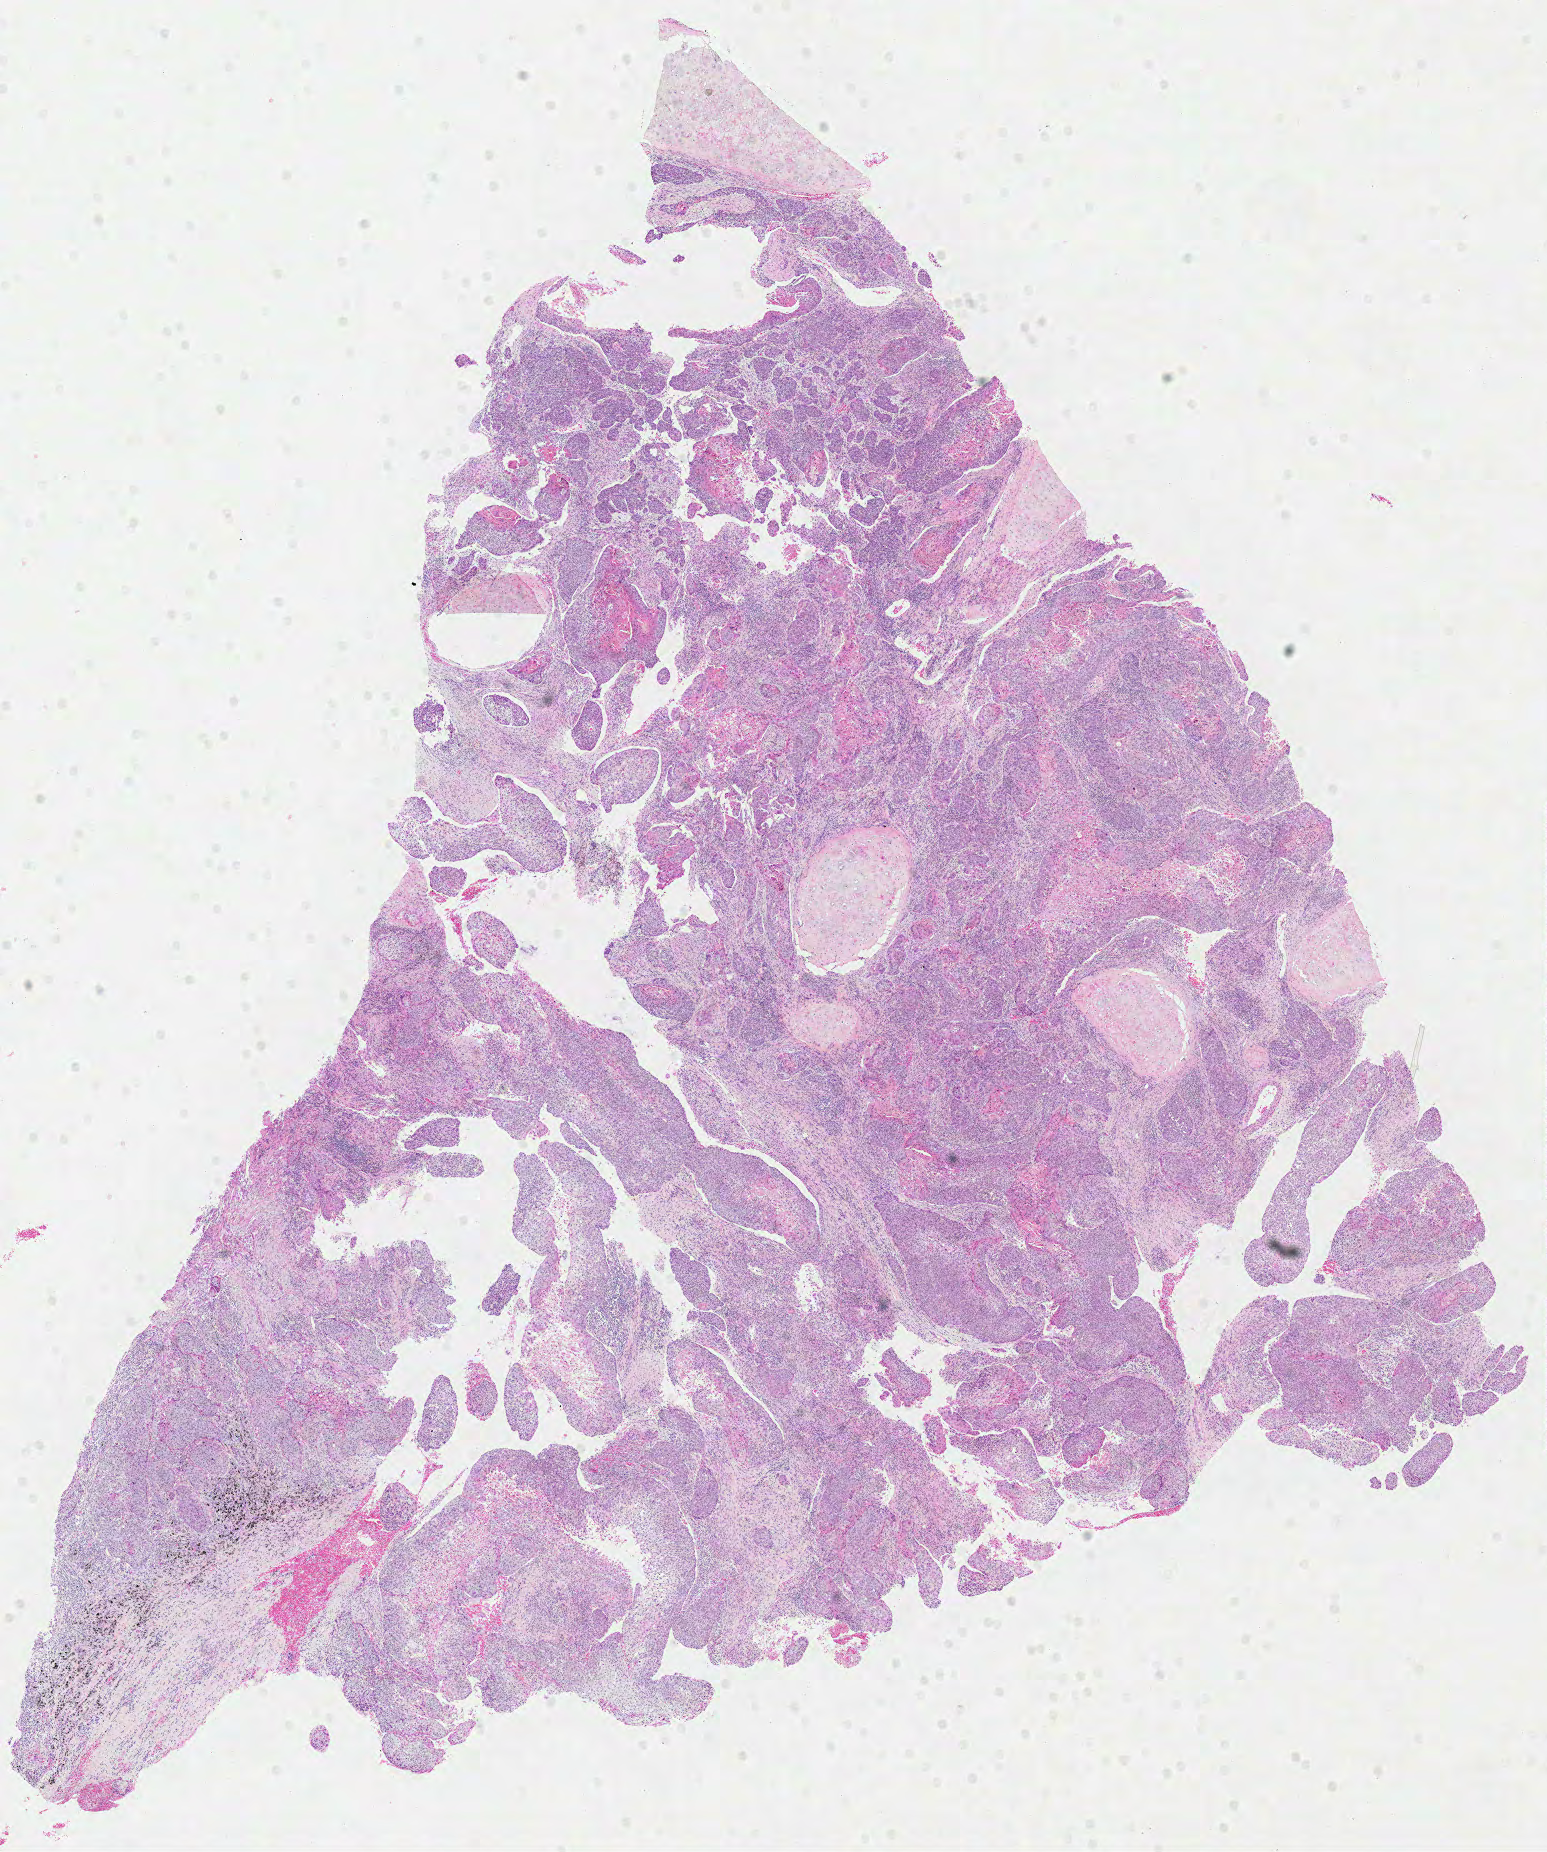
Digitized H&E tissue section (whole slide) — a low-resolution overview of the entire scanned area, about 12.2 x 14.6 mm. FFPE section. Primary tumour sample from the lung. Male patient; age at initial diagnosis 62 years.
Histologic diagnosis: Squamous cell carcinoma, NOS (lower lobe, lung). Laterality: right. AJCC pathologic stage: IIIB (6th edition). TNM: T2 N3 M0.